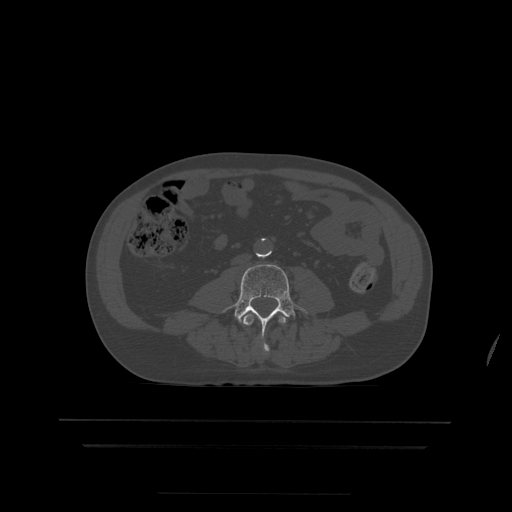
CT including the spine, one axial slice. Position 100 of 522 along the scan axis. Bone window (W 1800 / L 400 HU). 1.25 mm slice thickness. 512 × 512 image matrix, field of view 436 × 436 mm. Patient age 68 years. Case-level facts recorded for this patient, not image findings: primary cancer: urothelial.
Structures marked on this image (semi-automatically segmented with operator editing):
- L3 vertebra: box from (x=243, y=314) to (x=287, y=354) px
- L4 vertebra: (x=224, y=264)–(x=308, y=336)